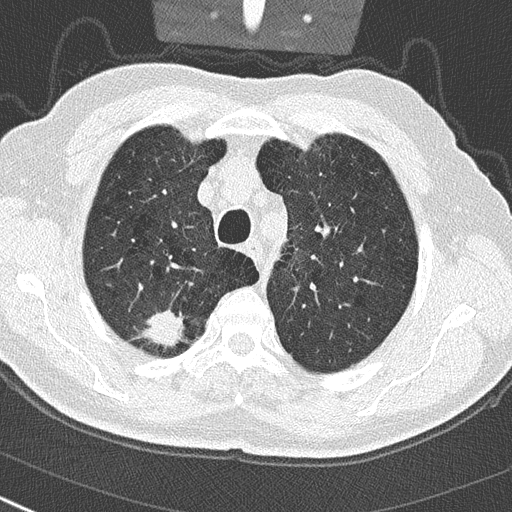
Low-dose screening chest CT, one axial slice. Position 232 of 290 along the scan axis. Reconstruction kernel B50f. Lung window (W 1500 / L -600 HU). 2 mm slice thickness. 512 × 512 image matrix, field of view 300 × 300 mm.
Structures marked on this image (outlined manually by an expert reader):
- lesion 1 (tumor, upper lobe of right lung): bounding box (x1, y1, x2, y2) in pixels: (142, 311, 185, 347)